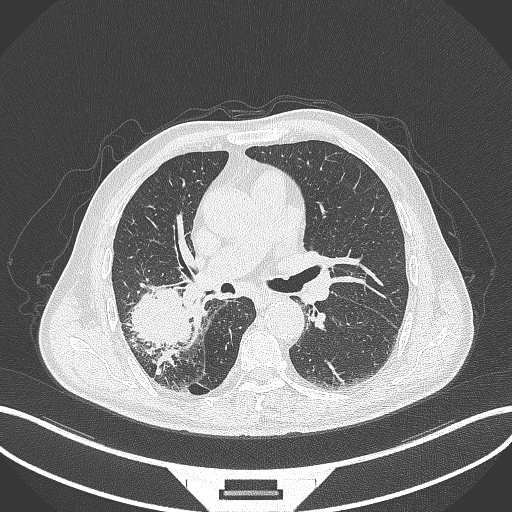
Chest CT, one axial slice; slice 235 of 429 in the series (ordered by position); reconstruction kernel B70f; 120 kVp; lung window (W 1500 / L -600 HU); 1 mm slice thickness; 512 × 512 image matrix, field of view 400 × 400 mm. Patient: male, 72 years. From the clinical record (not read from this slice): clinical TNM (as recorded): T3 N2 M0.
Structures marked on this image (bounding box drawn by a radiologist):
- lung tumour (recorded histology: adenocarcinoma): box from (x=125, y=282) to (x=193, y=354) px